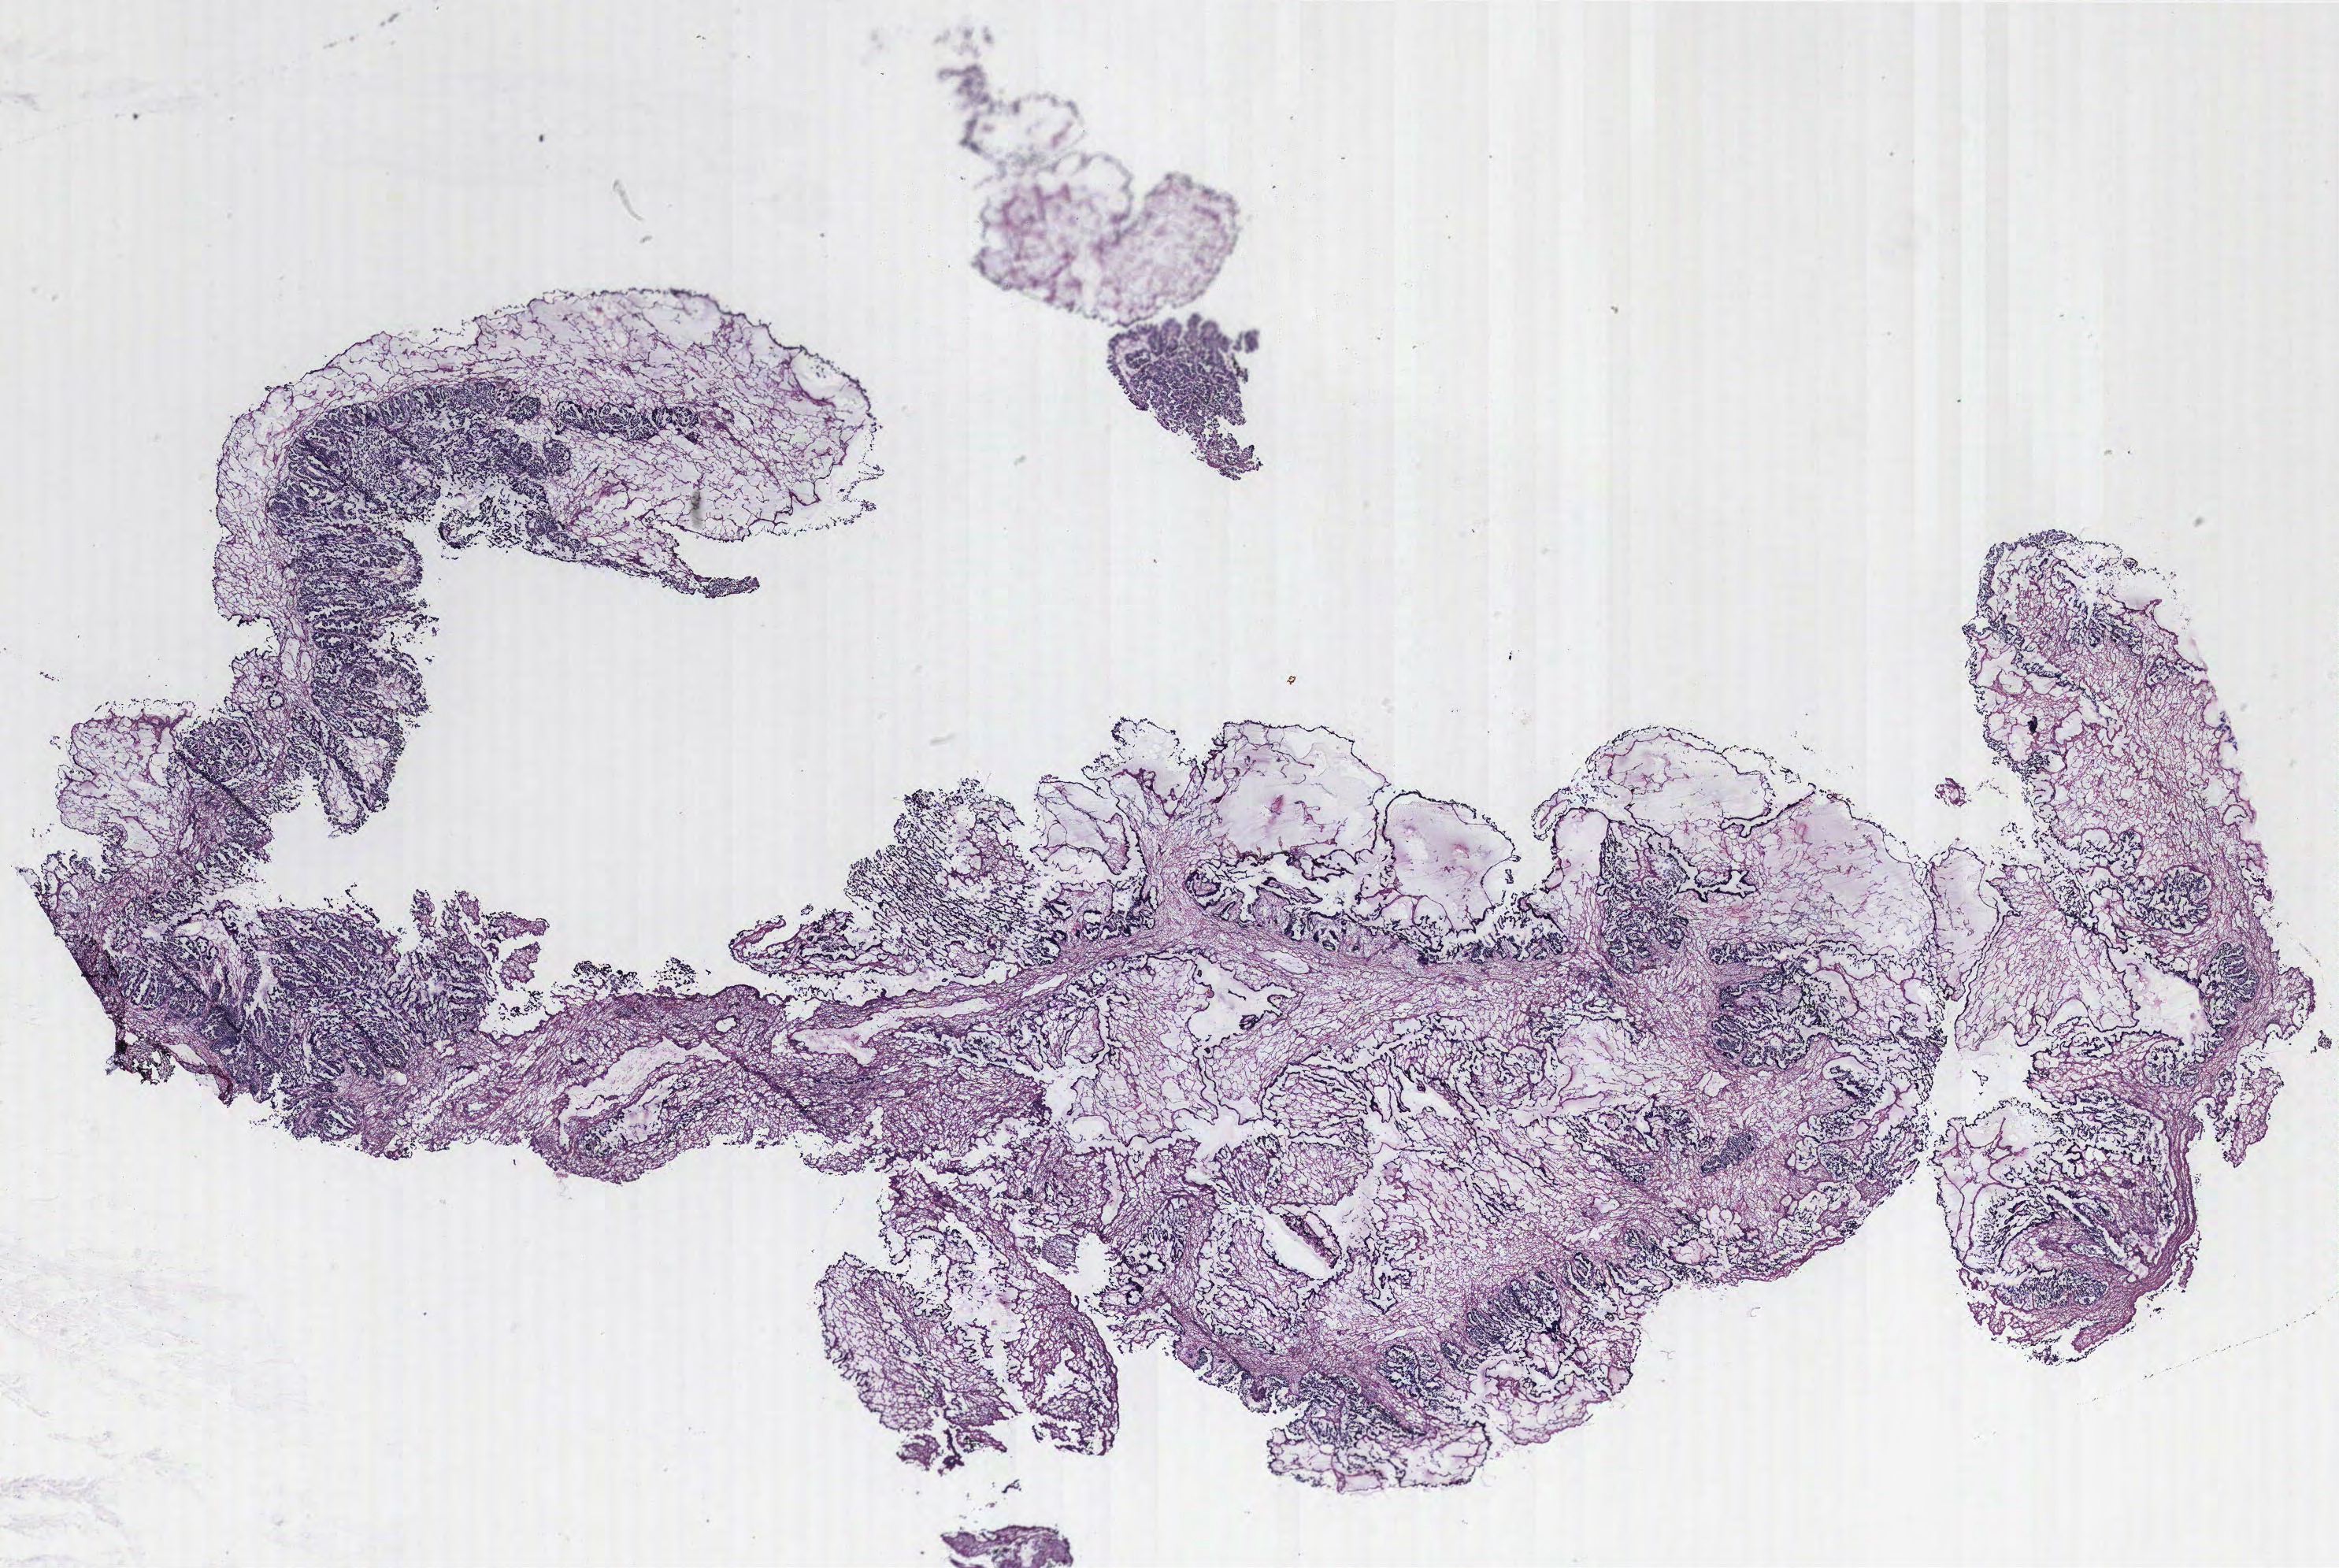
H&E whole-slide image — a low-resolution overview of the entire scanned area, about 23.8 x 15.9 mm (from a 40x scan). Tumour tissue sample, ovary. 79-year-old female patient.
Diagnosis: Serous adenocarcinoma, NOS. Primary tumour site (as recorded): ovary.